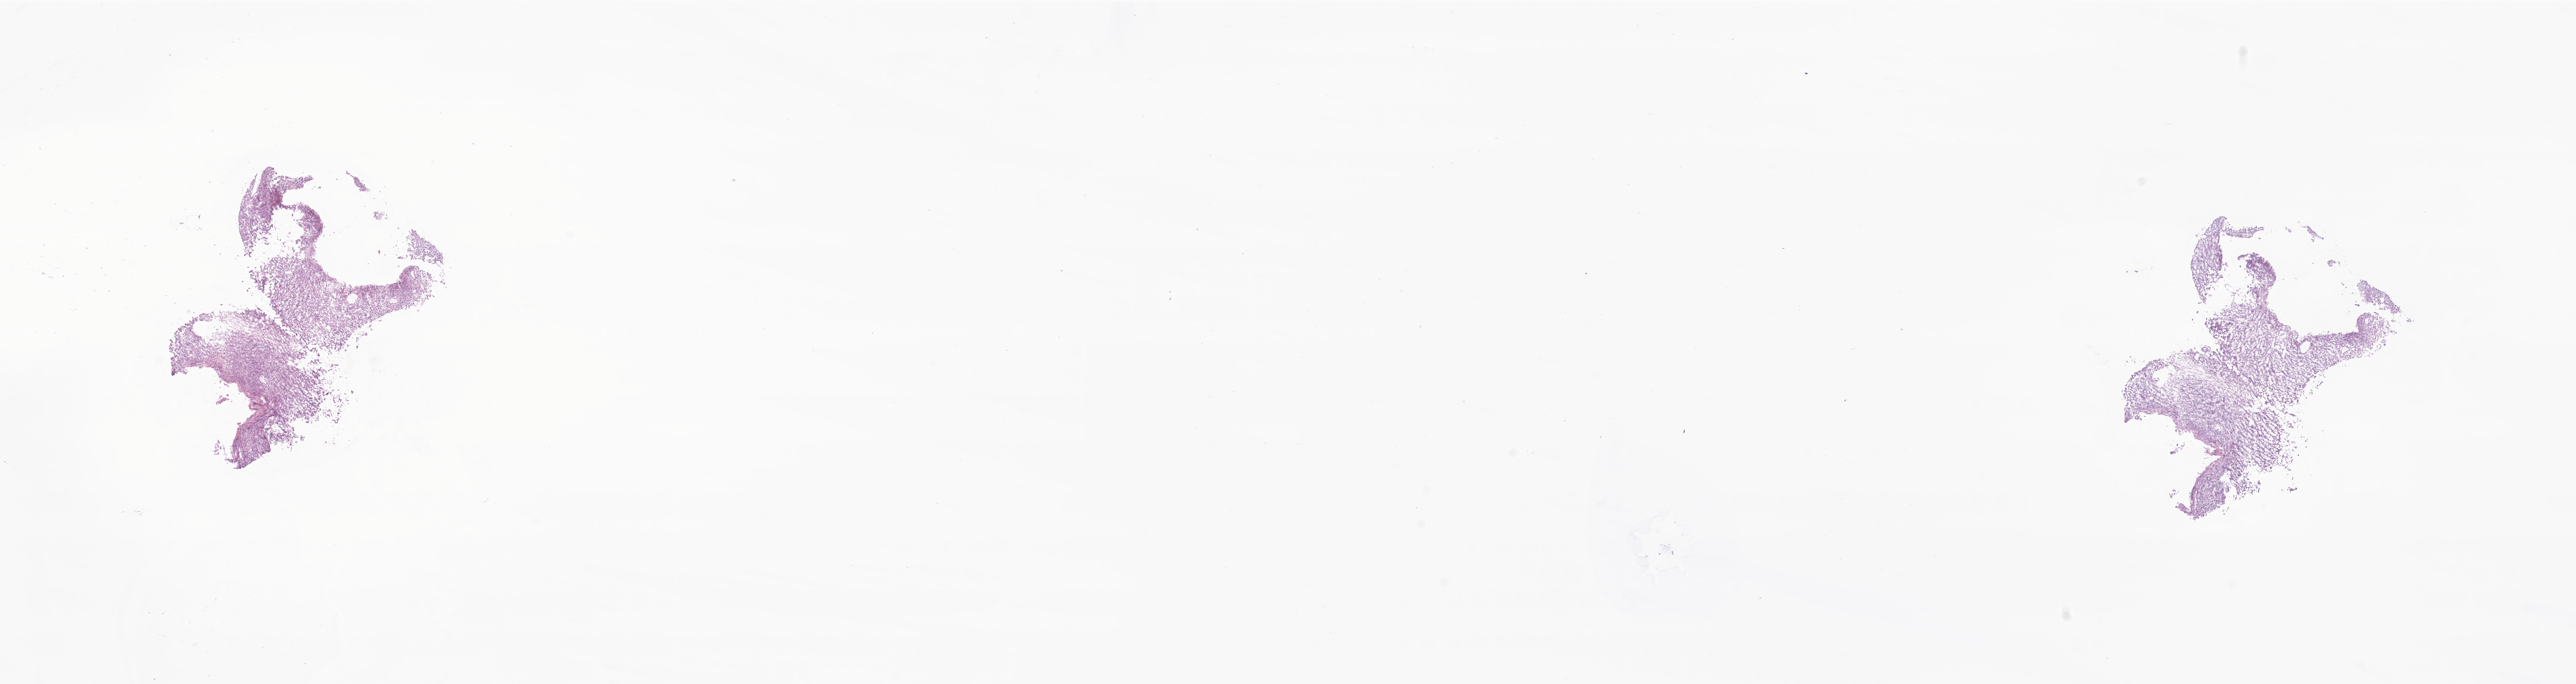
Whole-slide image, H&E stain of tumor tissue from the frontal lobe — a low-resolution overview of the entire scanned area, about 28.4 x 7.5 mm; cryosection (OCT / tissue freezing medium). Patient male; age 53 months (4 years 5 months).
Recorded diagnosis: Atypical teratoid/rhabdoid tumor.